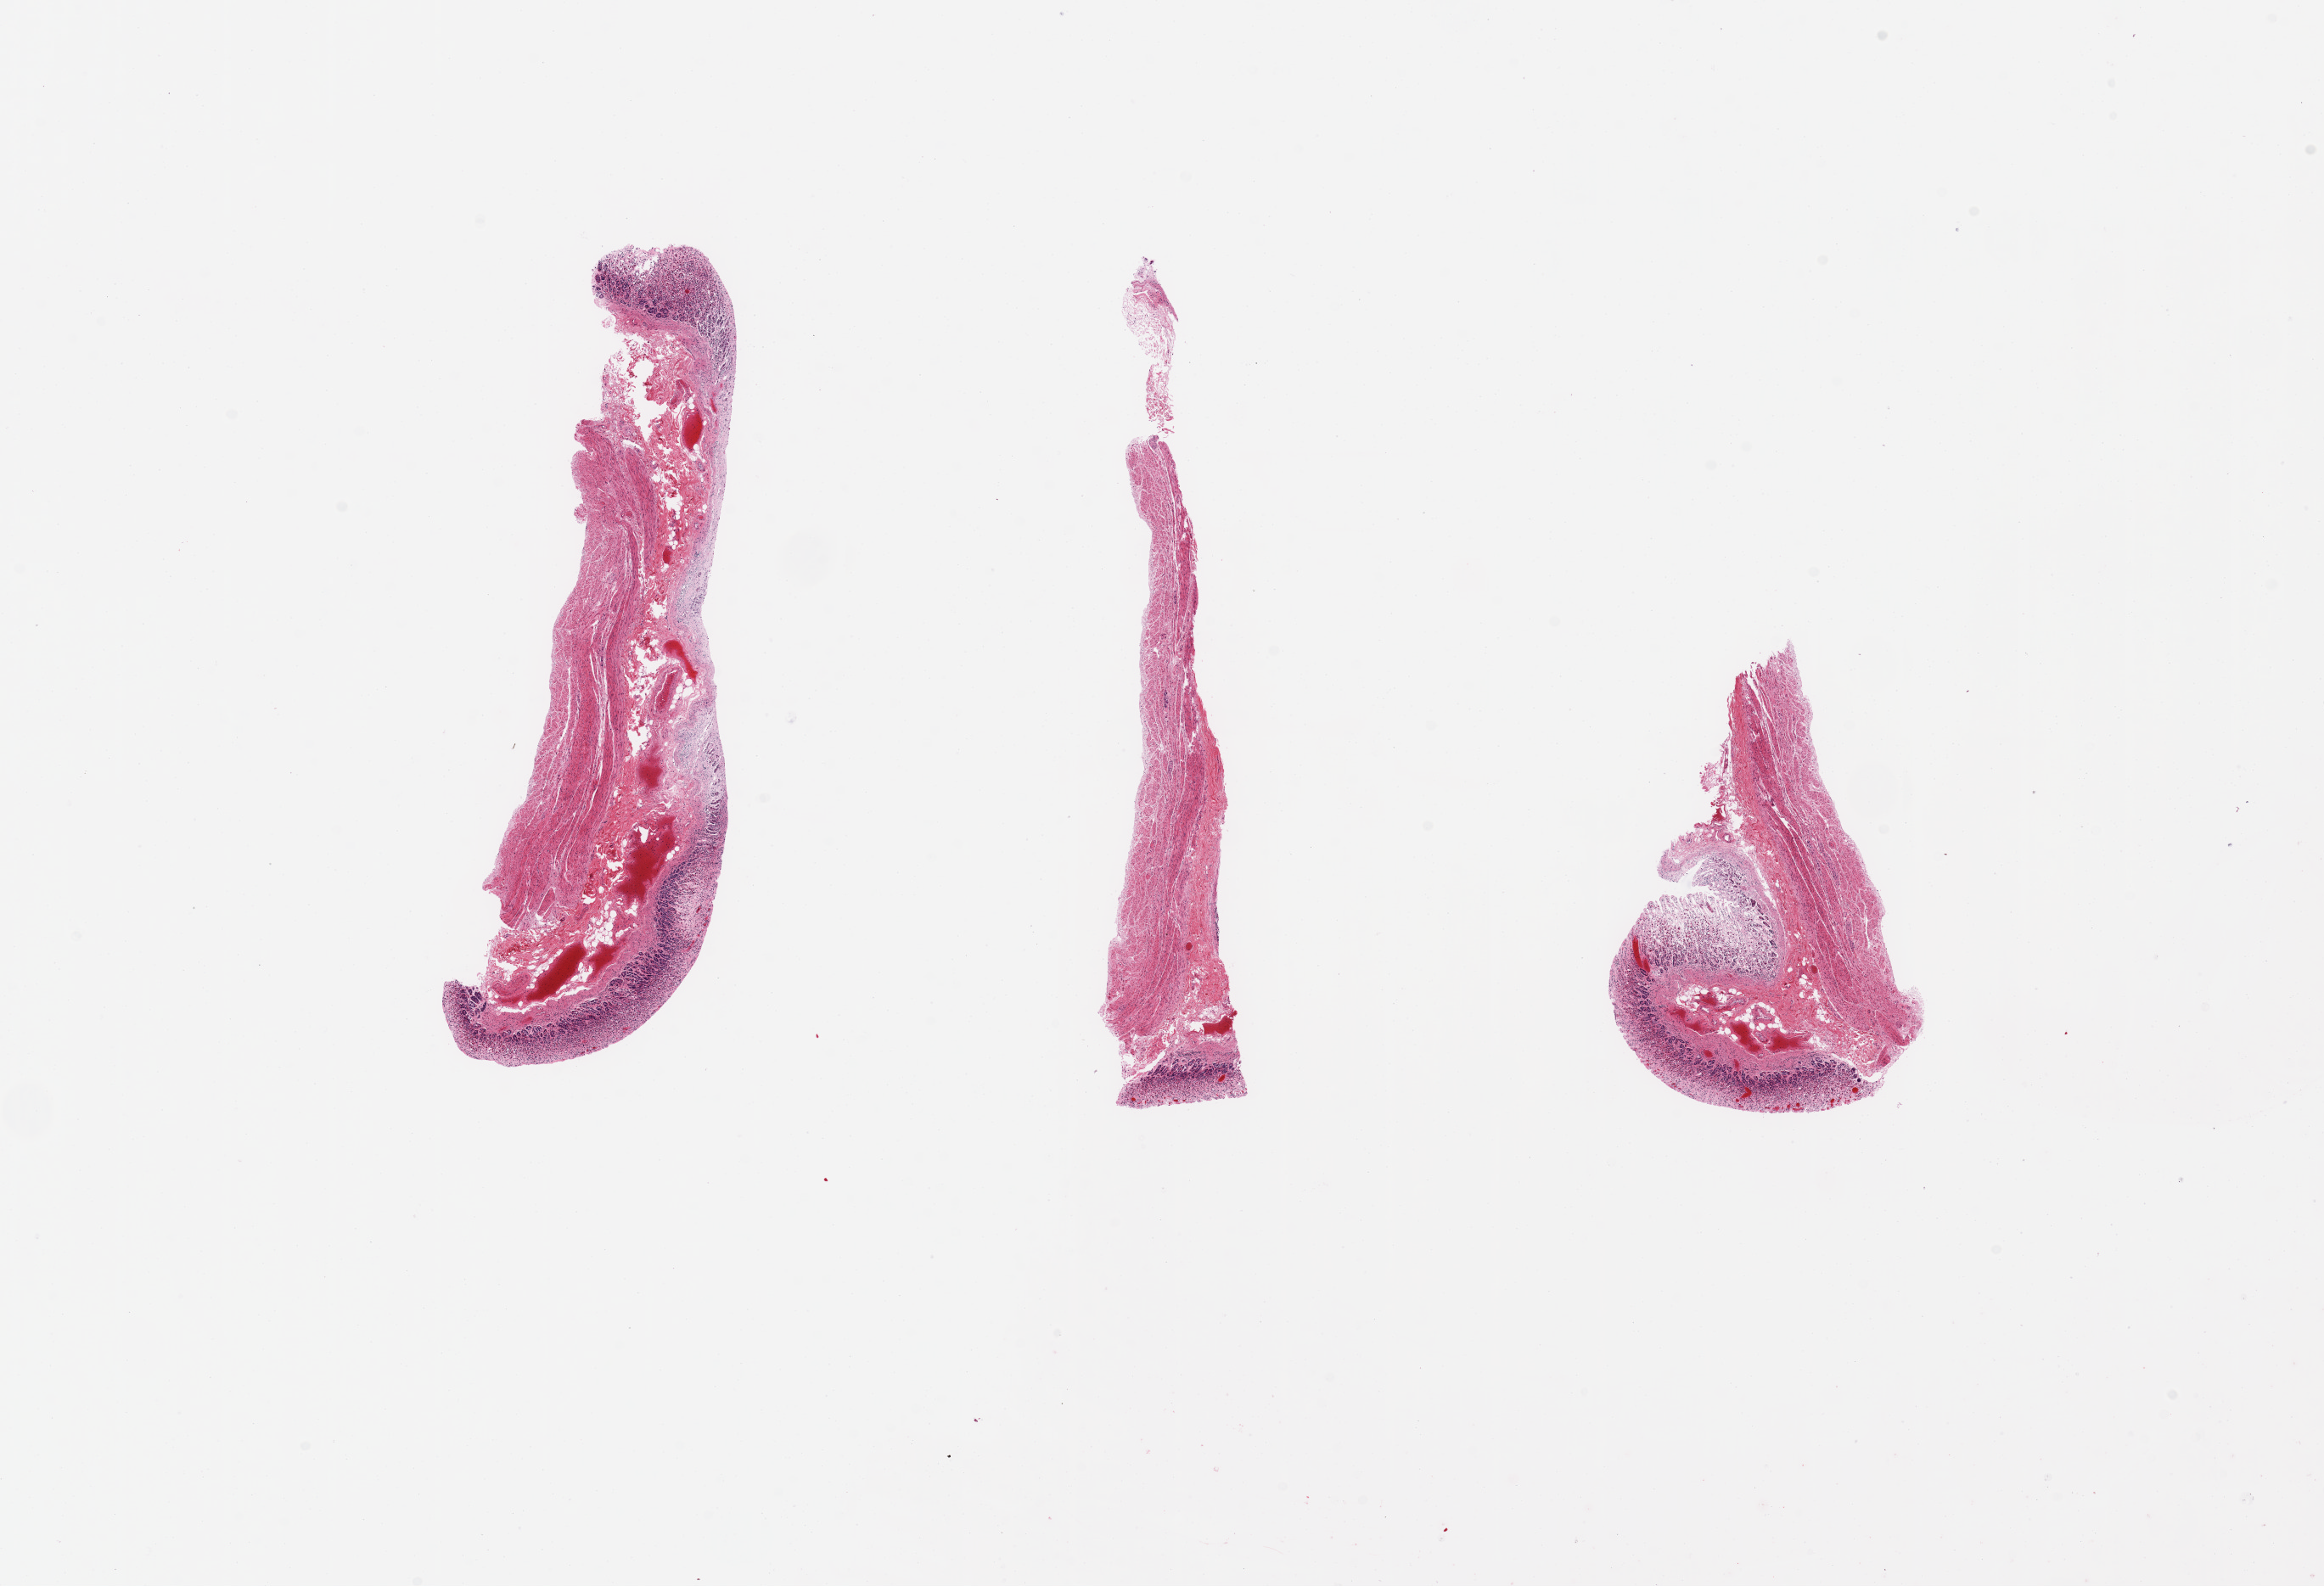
Whole-slide image, hematoxylin and eosin (H&E) stain, shown as a low-resolution overview of the whole scanned area (about 21.7 x 14.8 mm); PAXgene-fixed, paraffin-embedded tissue; section of stomach (target tissue); donor tissue sample. Donor: female.
Reviewer comment on this tissue sample: 3 pieces, 7x1.6 mm;Autolyzed superficial 2/3 mucosa.